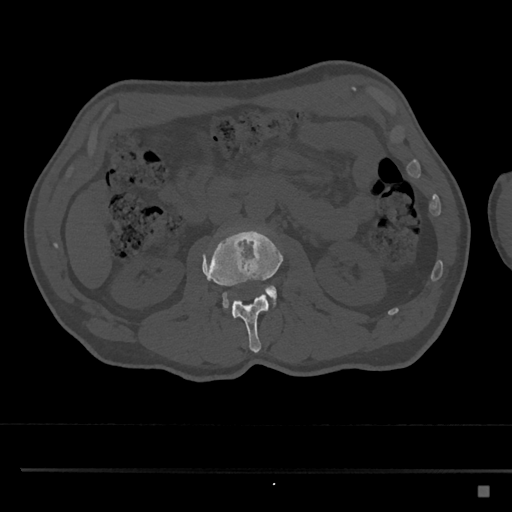
CT including the spine, one axial slice; slice 741 of 797 in the series (ordered by position); reconstruction kernel Br40s/3; 120 kVp; bone window (W 1800 / L 400 HU); 0.5 mm slice thickness; 512 × 512 image matrix. Patient: male, 59 years. From the clinical record (not read from this slice): primary cancer: prostate.
Structures marked on this image (semi-automatic segmentation, software-assisted and operator-edited):
- L2 vertebra: bounding box [x1, y1, x2, y2] px = [202, 228, 283, 353]
- L3 vertebra: [222, 285, 277, 310]